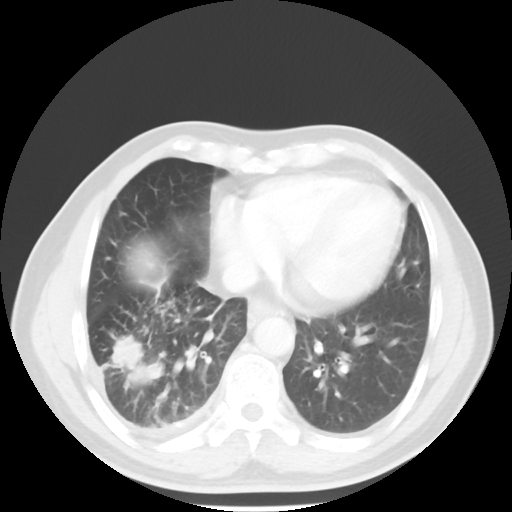
Chest CT, one axial slice; slice 19 of 56 in the series (ordered by position); reconstruction kernel STANDARD; 120 kVp; lung window (W 1500 / L -600 HU); 5 mm slice thickness; 512 × 512 image matrix. Patient: male, 56 years. Case-level facts recorded for this patient, not image findings: clinical TNM (as recorded): T2 N3 M1.
Annotated regions visible in this slice (rectangle marked by the reading radiologist):
- lung tumour (recorded histology: adenocarcinoma): box from (x=107, y=329) to (x=161, y=384) px